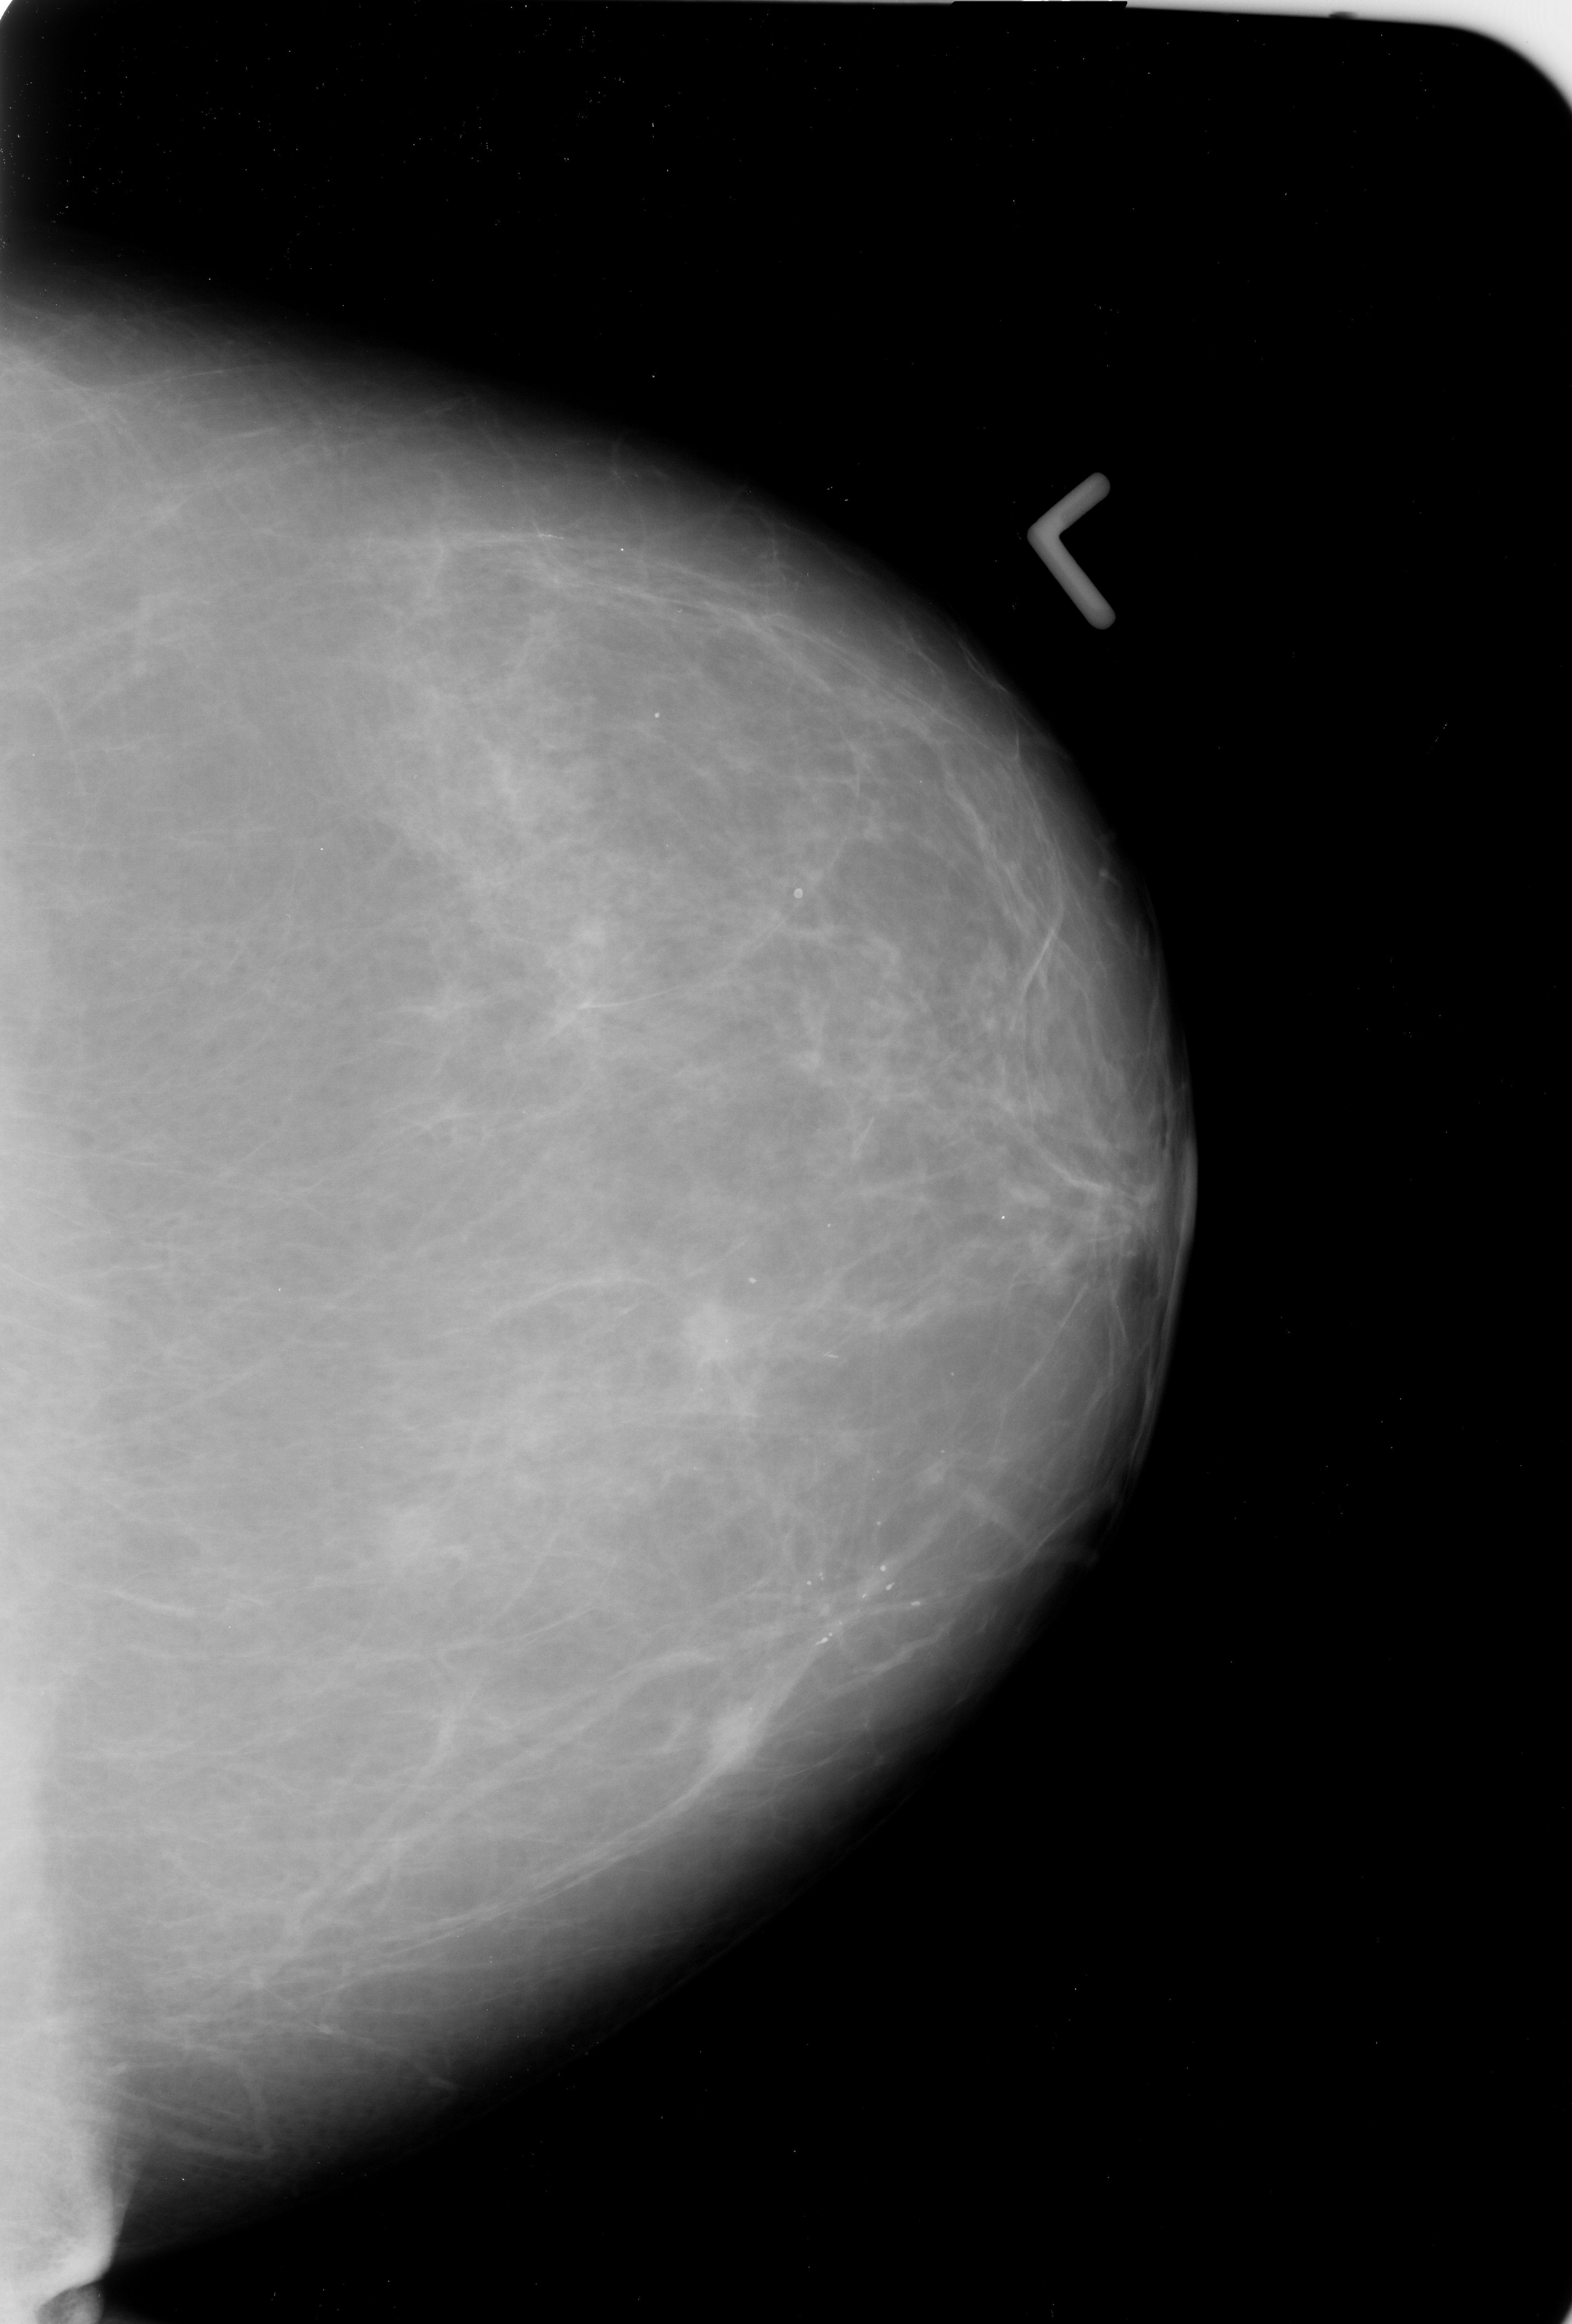
Scanned film-screen mammogram; left breast; CC view; breast composition: almost entirely fatty (BI-RADS density category 1 of 4); 1572 × 2324 image matrix.
Marked abnormalities (boxes around the expert regions of interest):
- Finding 1 of 2: mass, shape irregular, margins spiculated; BI-RADS assessment category 4; subtlety rating 3 on a 1 (subtle) to 5 (obvious) scale; pathology (as recorded): malignant: box from (x=664, y=1283) to (x=752, y=1381) px
- Finding 2 of 2: mass, shape irregular, margins spiculated; BI-RADS assessment category 4; pathology (as recorded): malignant: (x=700, y=1699)–(x=771, y=1784)